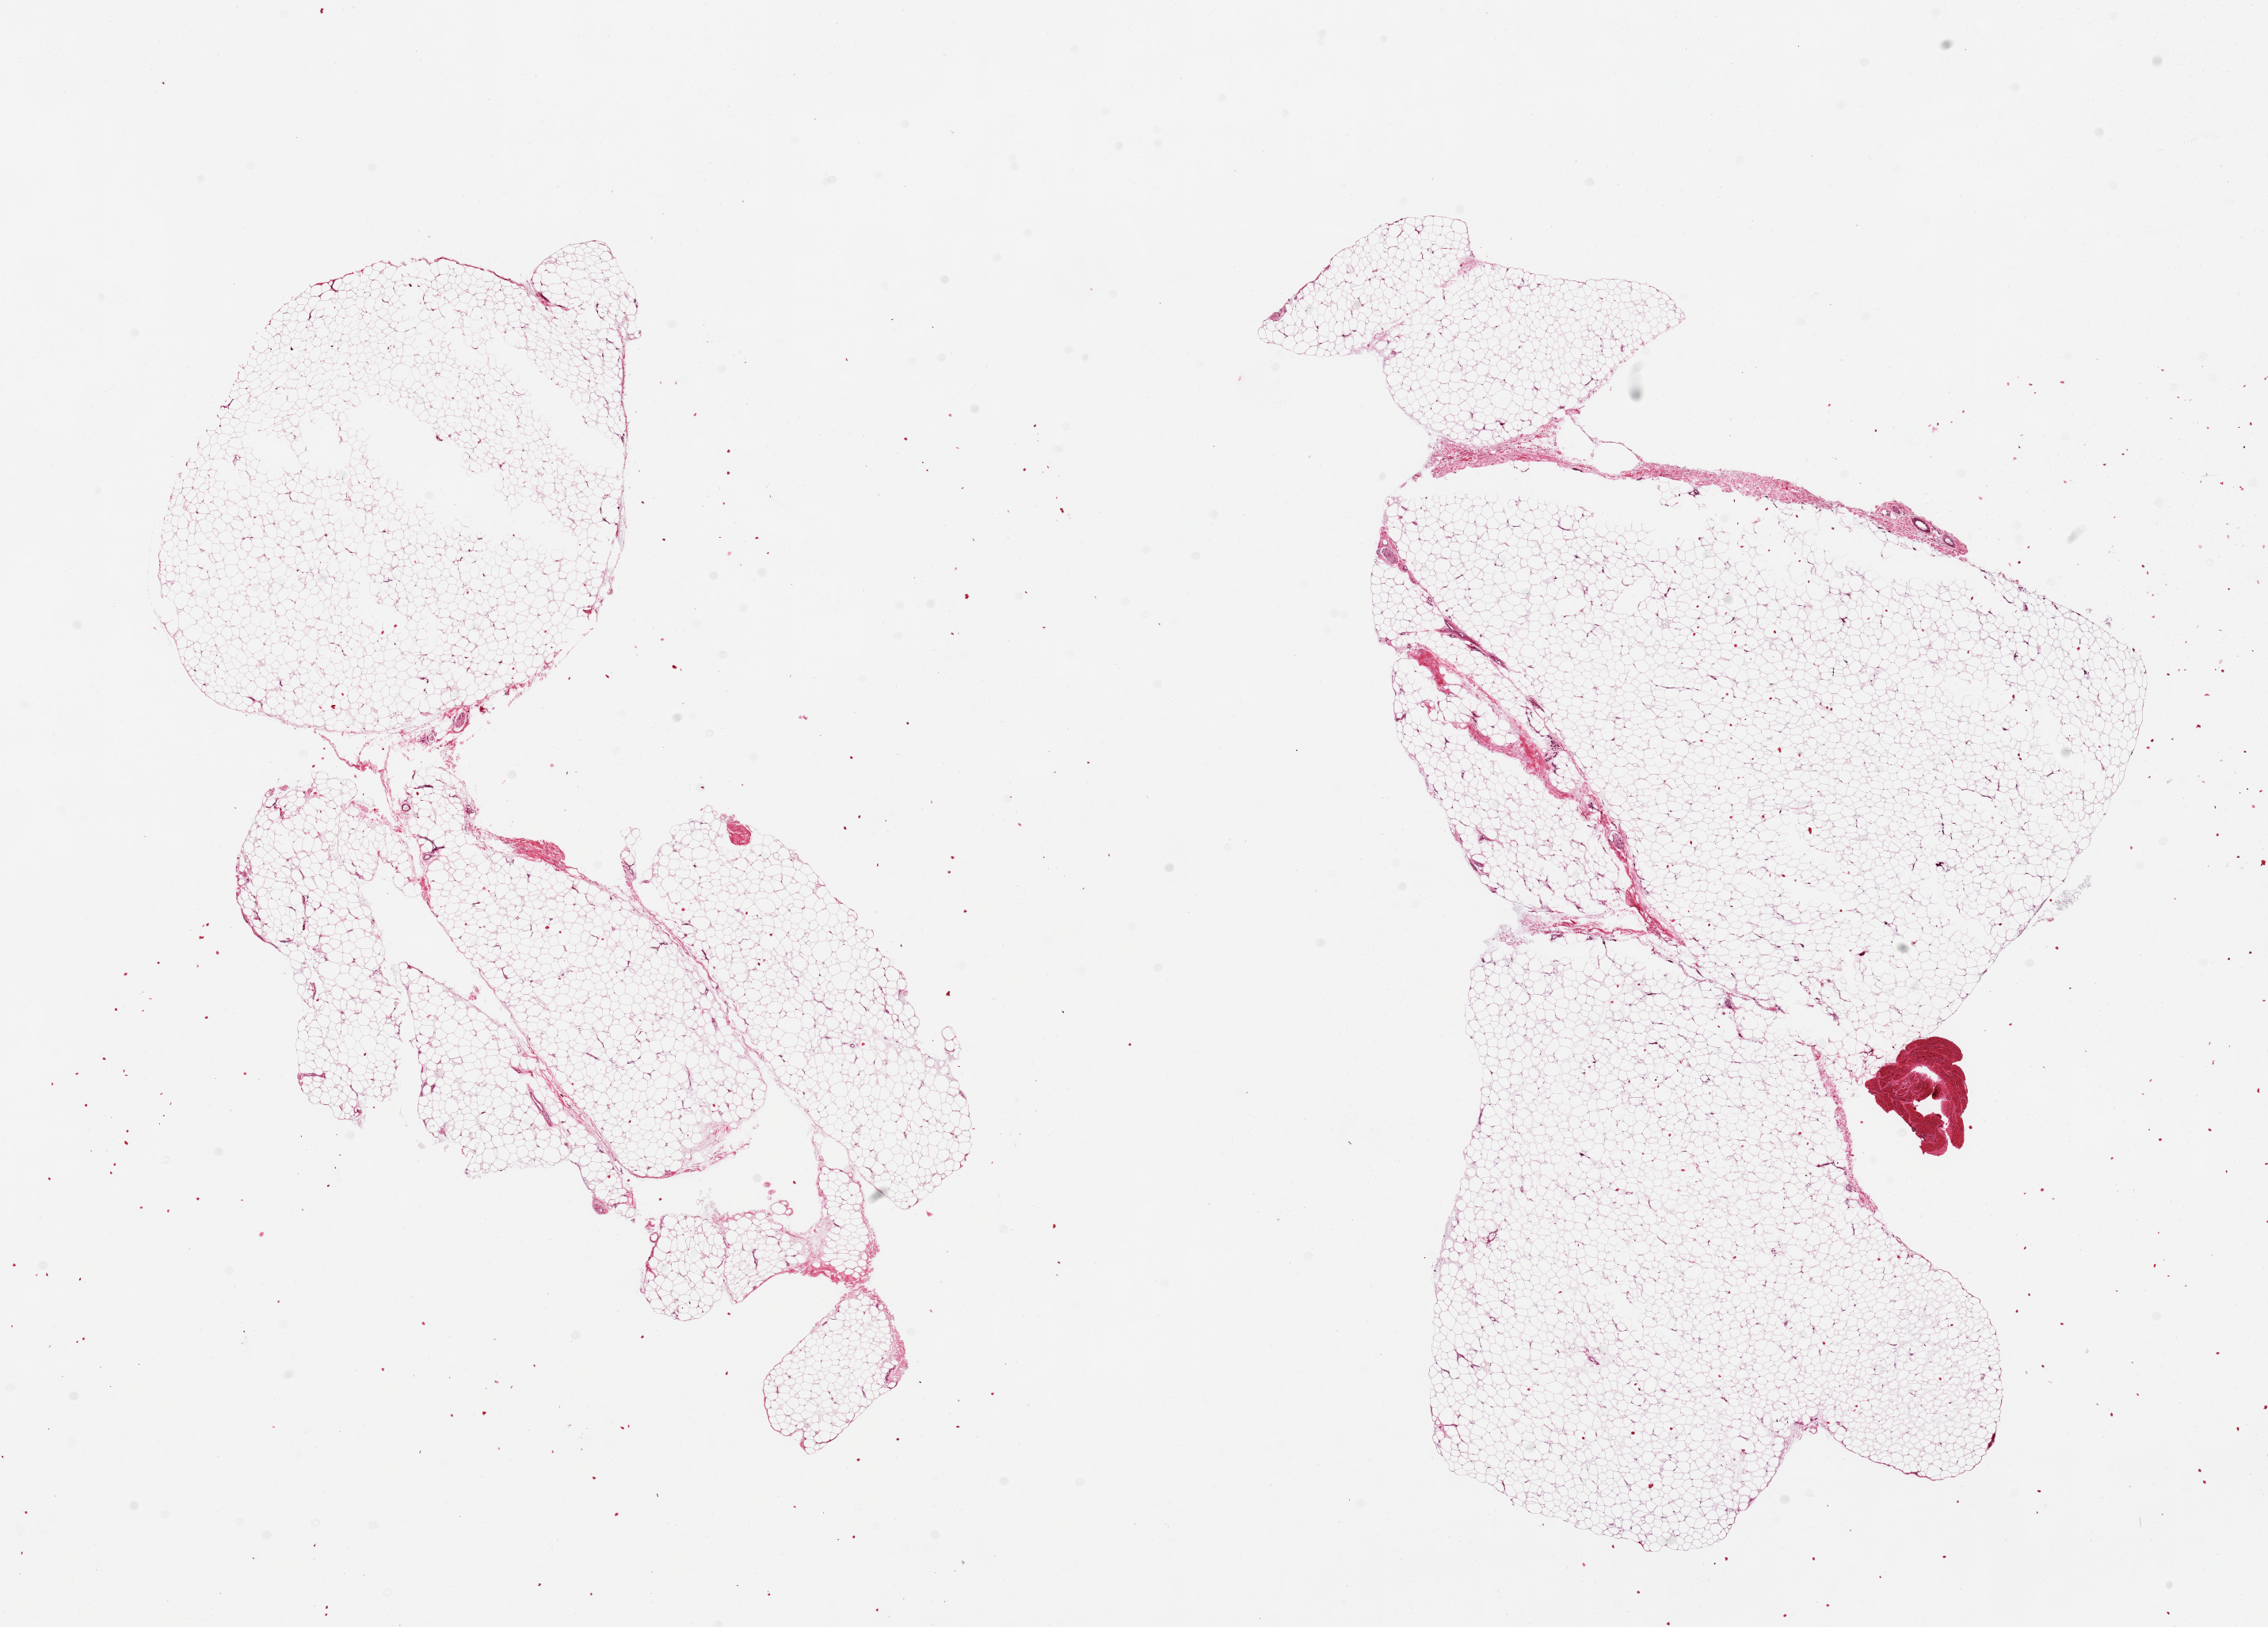
H&E whole-slide image — whole scanned area (about 22.6 x 16.2 mm) shown as a low-resolution overview. PAXgene-fixed paraffin-embedded (PFPE) section. Target tissue: adipose tissue. Donor tissue sample. Donor sex: male.
• pathologist's review note for this sample: 2 pieces; 1mm smooth muscle carry-over